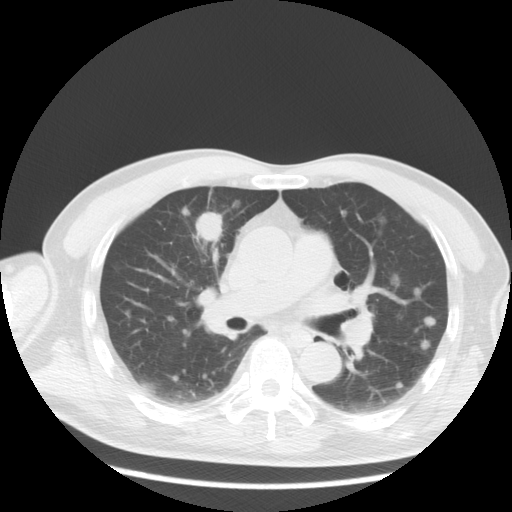
Chest CT, one axial slice; slice 11 of 36 in the series (ordered by position); reconstruction kernel STANDARD; 120 kVp; lung window (W 1500 / L -600 HU); 5 mm slice thickness; 512 × 512 image matrix, field of view 369 × 369 mm. Patient: male, 57 years. Case-level facts recorded for this patient, not image findings: clinical TNM (as recorded): T2 N3 M1a.
Outlined on this slice (rectangle marked by the reading radiologist):
- lung tumour (recorded histology: adenocarcinoma): bounding box [x1, y1, x2, y2] px = [192, 208, 224, 246]